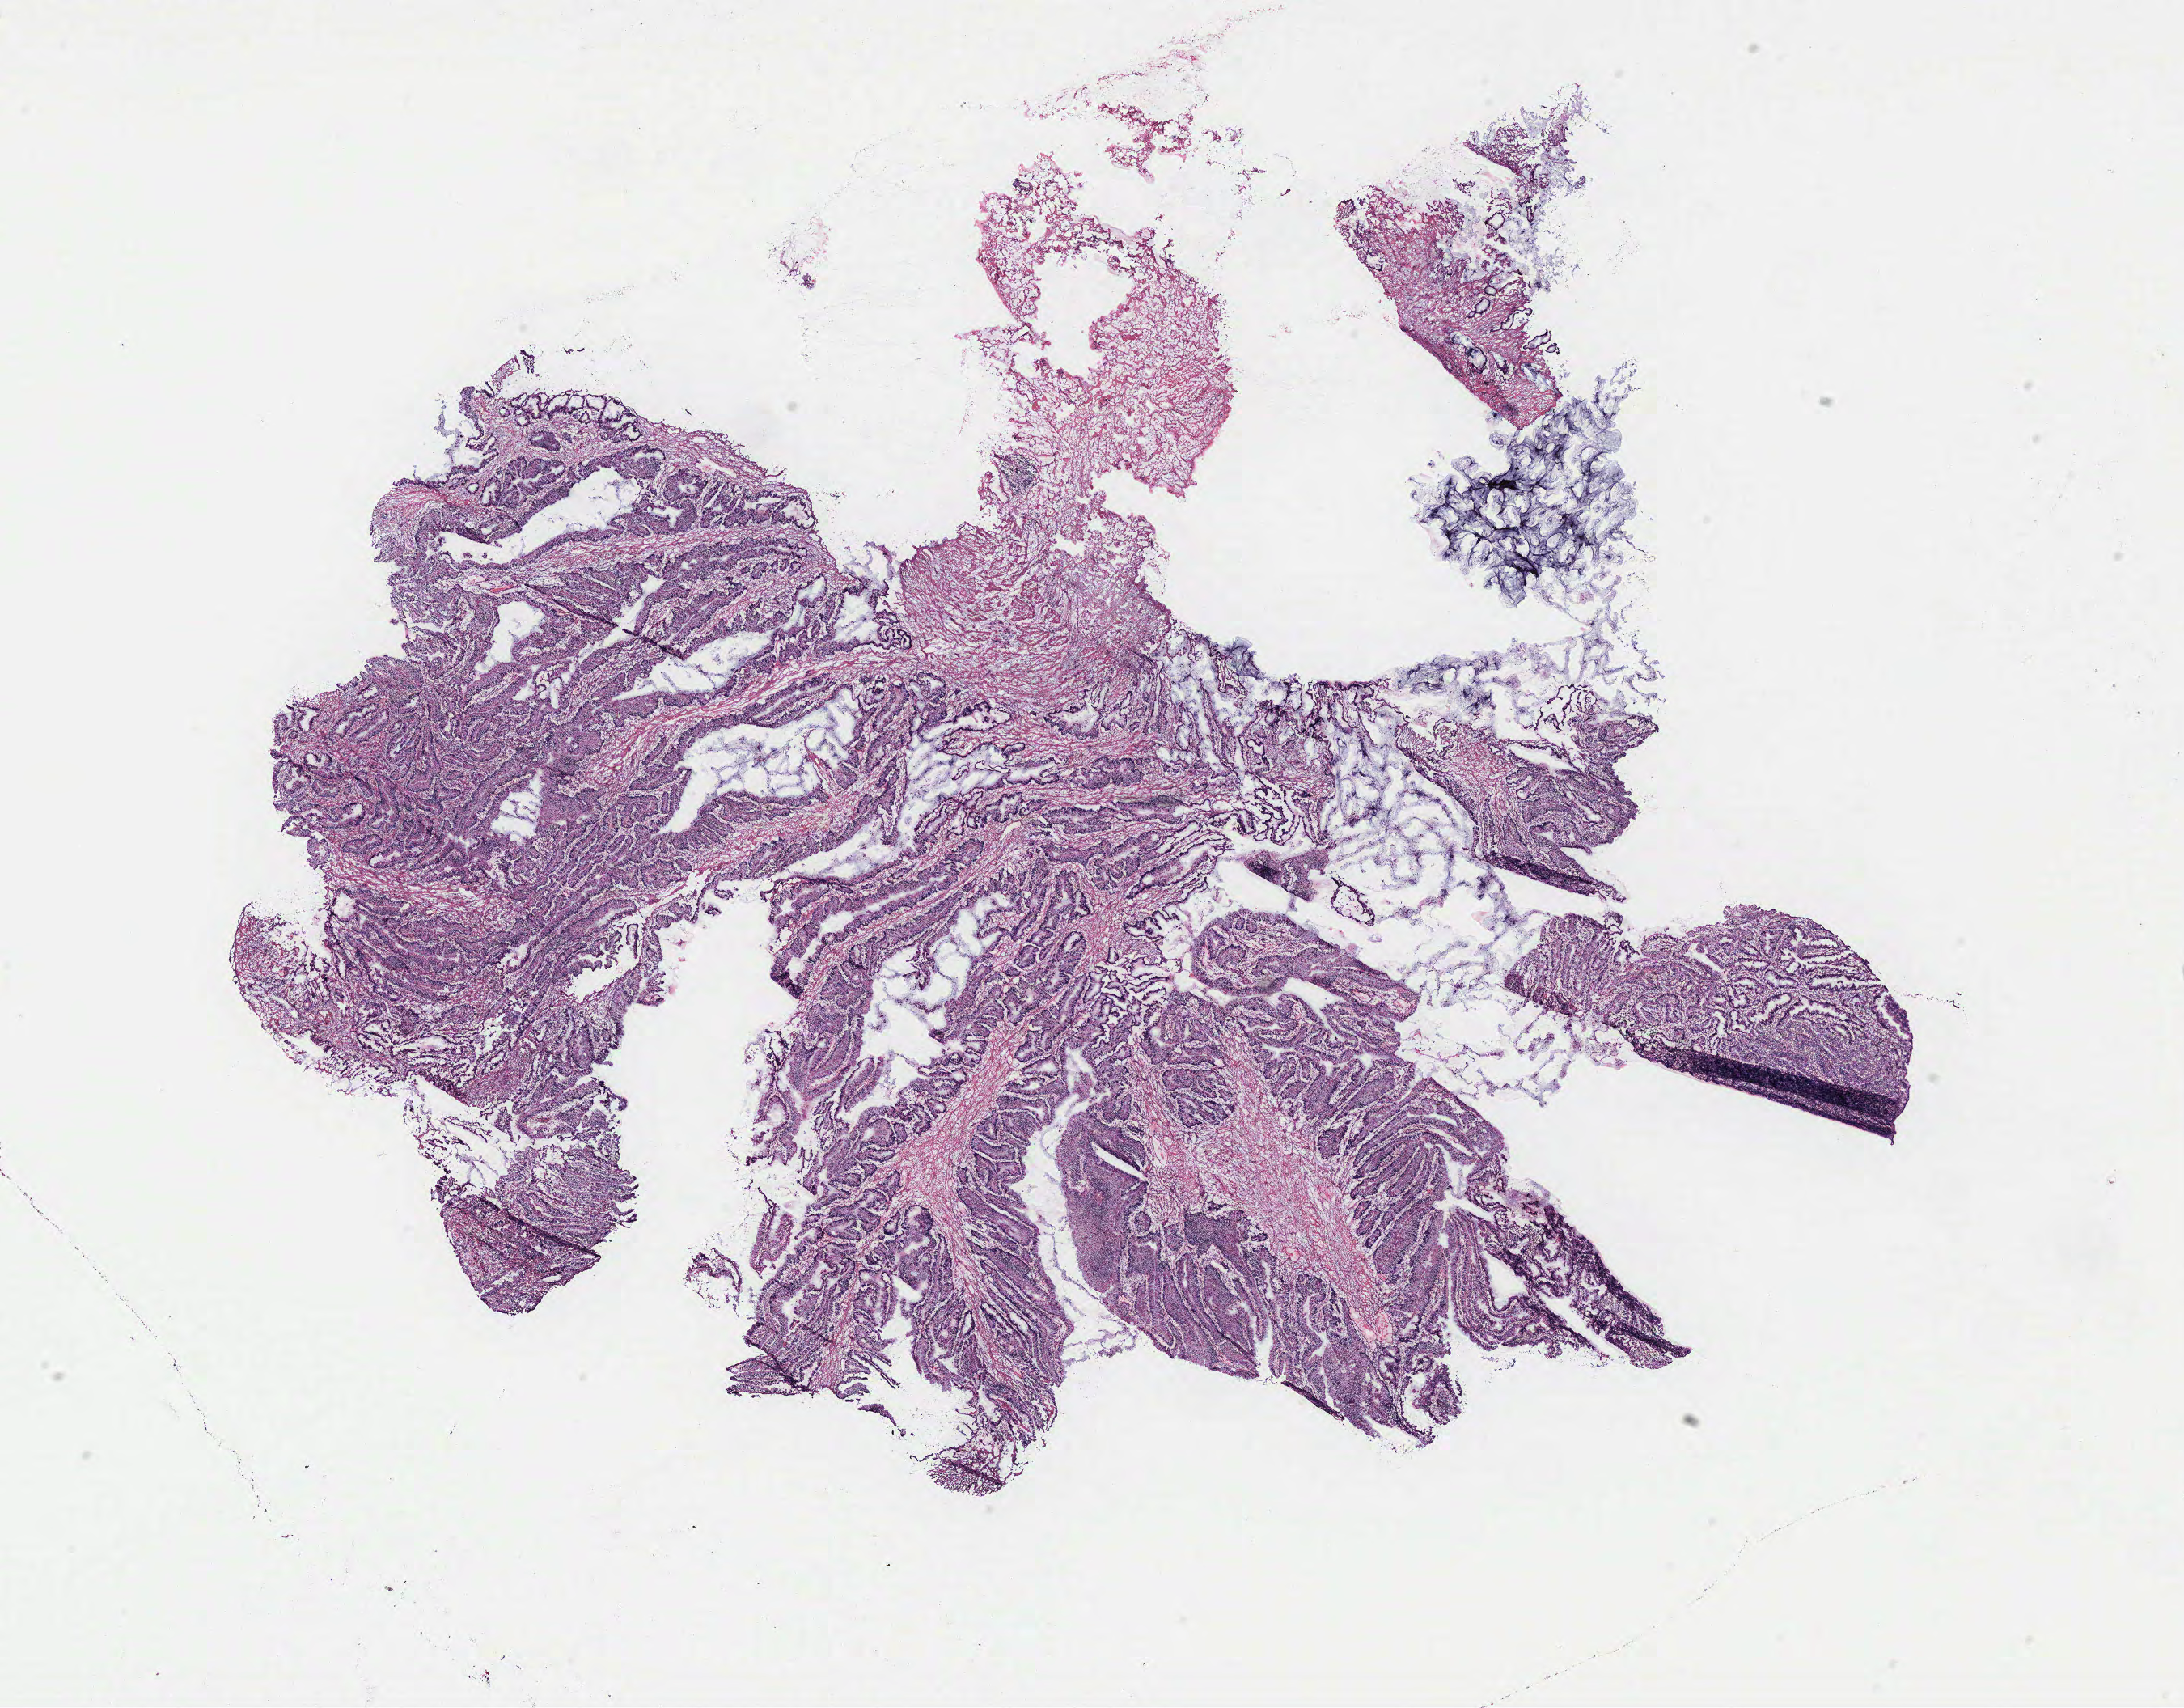
Digitized Hematoxylin and eosin (H&E) stained tissue section (whole slide) — whole scanned area (about 21.6 x 16.9 mm, slide scanned at 40x) shown as a low-resolution overview. Colon, tissue type not recorded. Male patient.
Patient diagnosis: Adenocarcinoma, NOS.